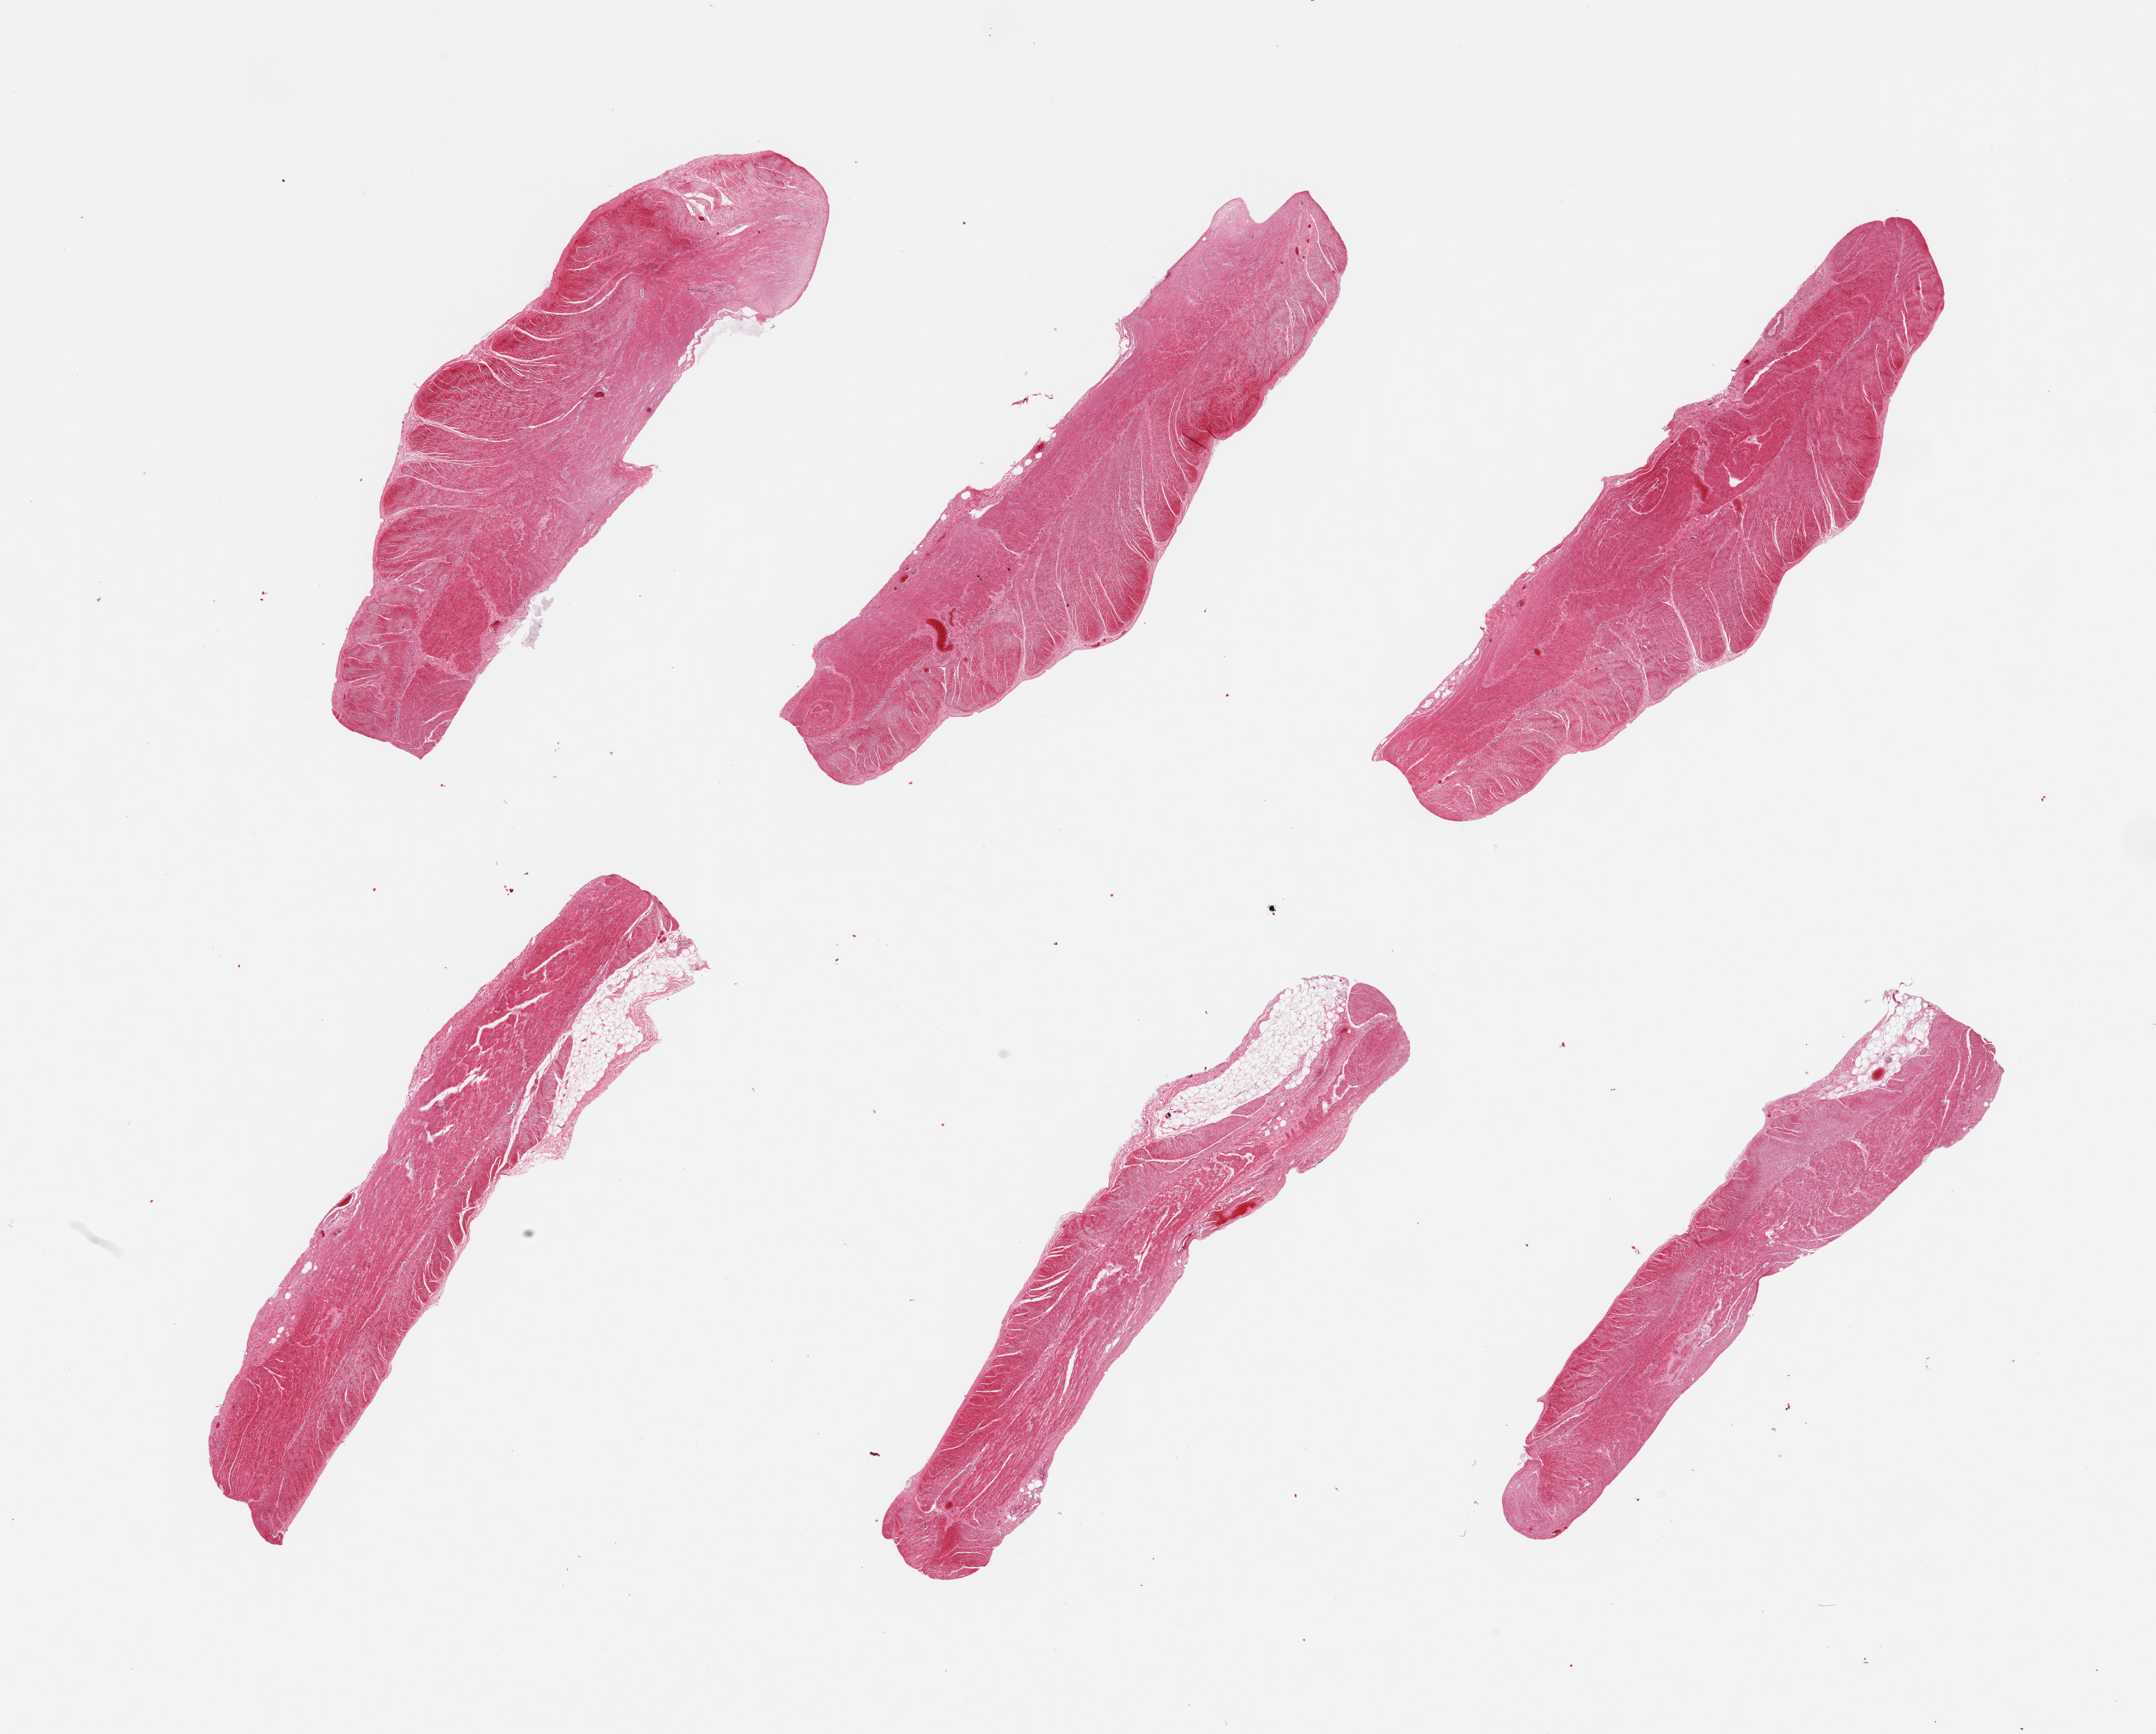
Digitized hematoxylin and eosin (H&E)-stained section — low-resolution overview of the scanned area, about 24.6 x 19.8 mm; PAXgene-fixed, paraffin-embedded tissue; sampled site (target tissue): sigmoid colon; donor tissue sample.
Reviewer comment on this tissue sample: 6 pieces, confirmed target muscularis, nubbins of adherent fat up to ~0.6mm.